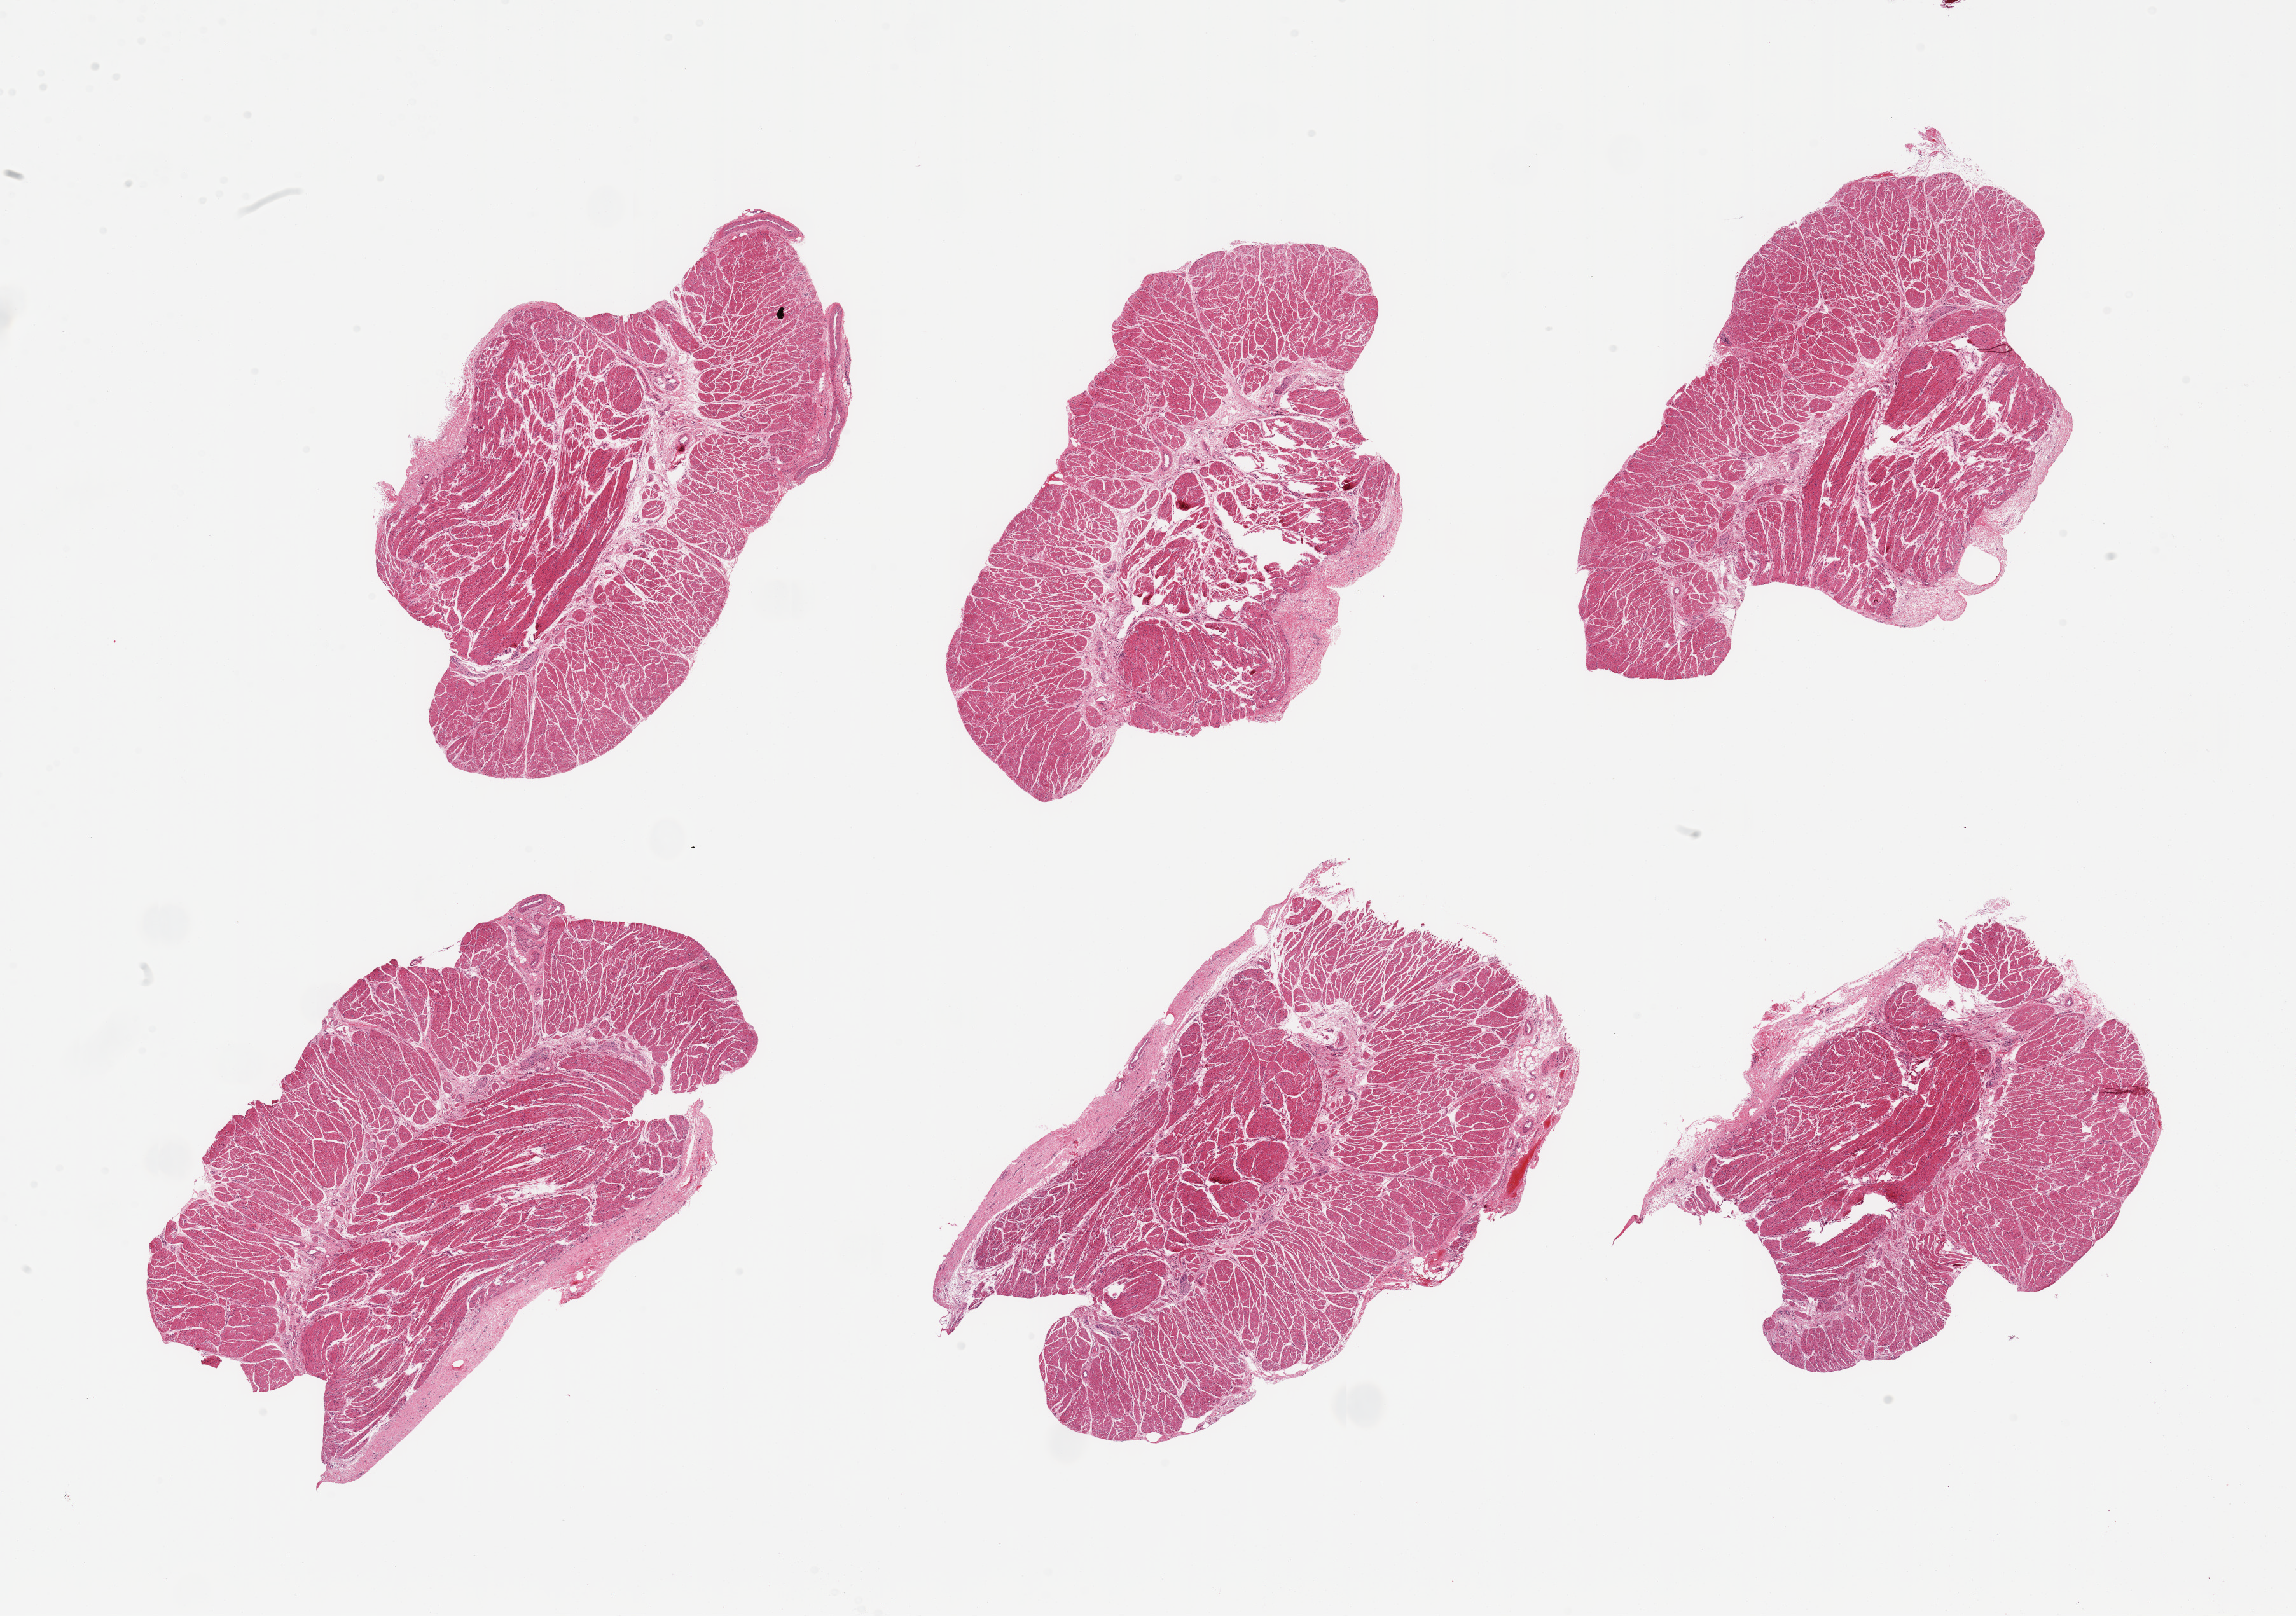
Haematoxylin and eosin whole-slide image, low-resolution overview of the scanned area, about 28.5 x 20.1 mm. PAXgene-fixed, paraffin-embedded tissue. Target tissue: esophageal muscle. Donor tissue sample. Donor: male.
- reviewer comment on this tissue sample: 6 pieces, confirmed target muscularis